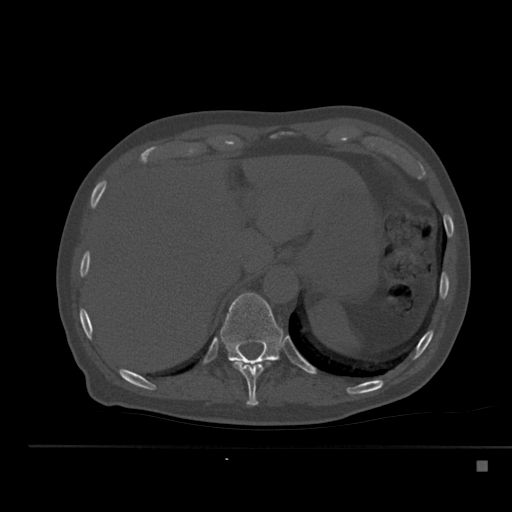
CT including the spine, one axial slice. Position 257 of 517 along the scan axis. Reconstruction kernel Br40s. Bone window (W 1800 / L 400 HU). 512 × 512 image matrix, field of view 408 × 408 mm. Male patient, age 70 years. Case-level facts recorded for this patient, not image findings: primary cancer: renal.
Structures marked on this image (semi-automatically segmented with operator editing):
- T10 vertebra: box from (x=233, y=360) to (x=271, y=406) px
- T11 vertebra: (x=217, y=292)–(x=286, y=364)